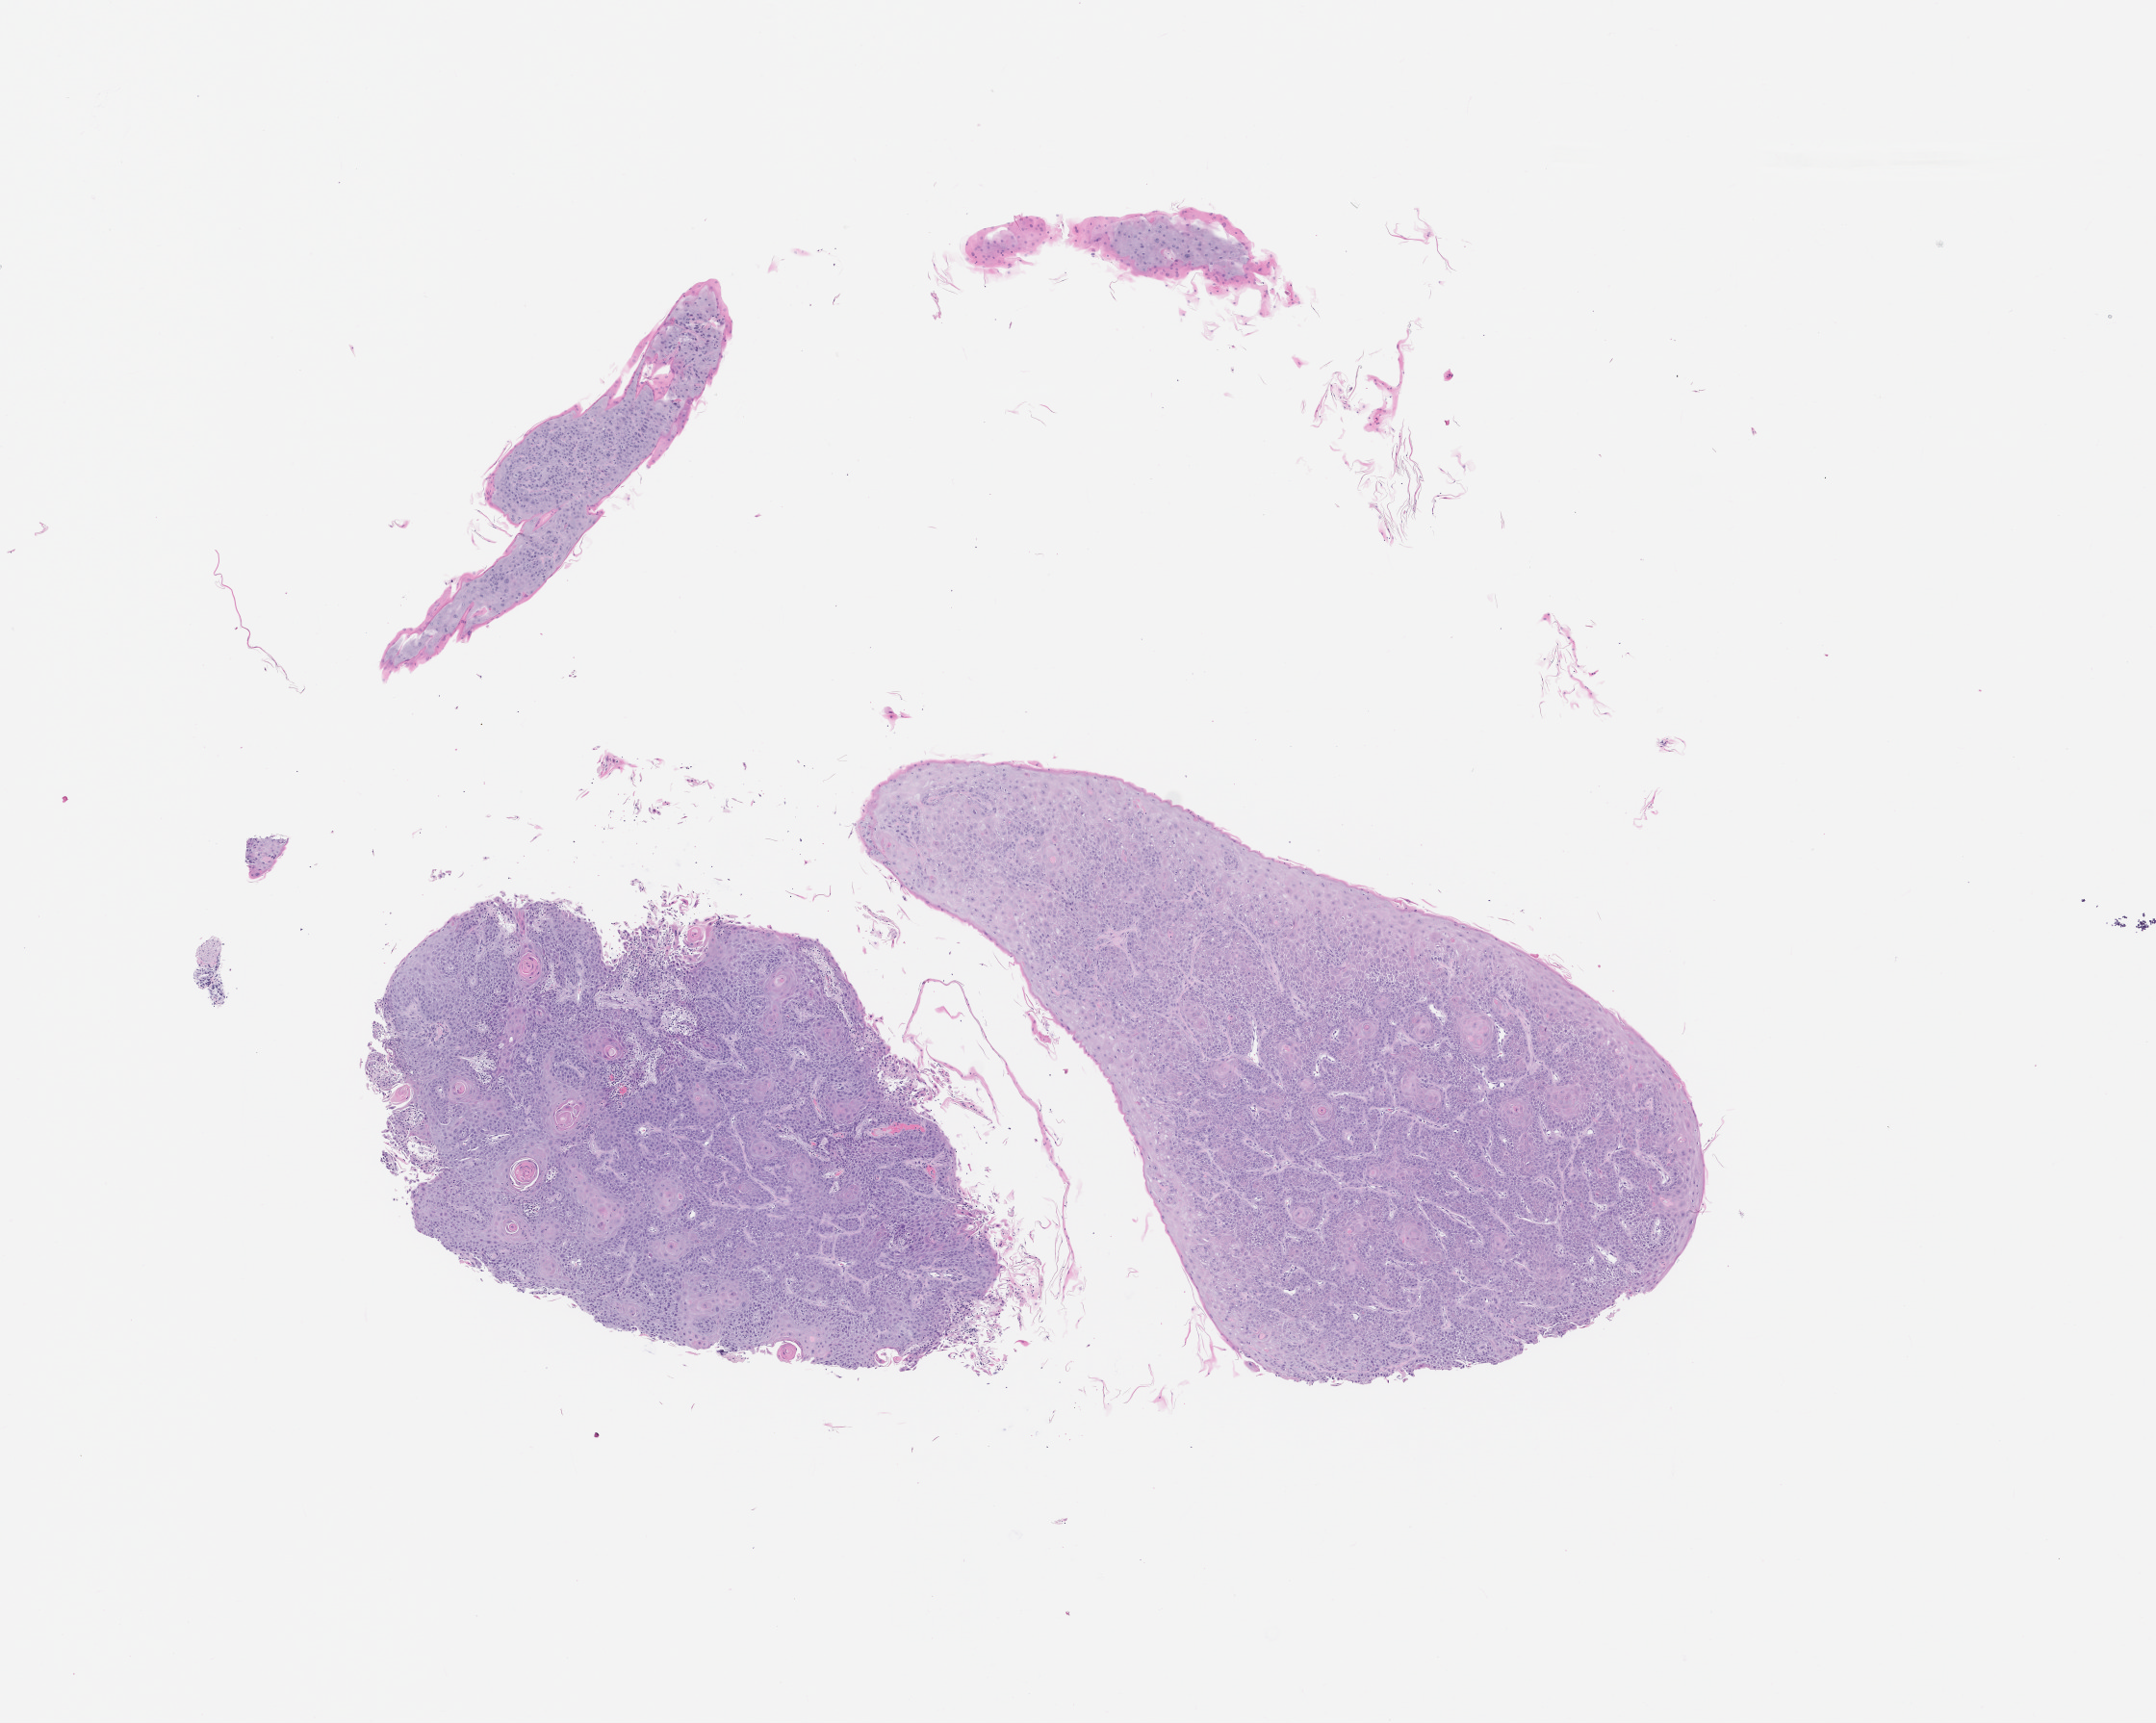
Hematoxylin and eosin (H&E) whole-slide image of a patient-derived xenograft (PDX) tumor grown in a mouse, passage 0, whole scanned area (about 9.0 x 7.2 mm) shown as a low-resolution overview. Formalin-fixed, paraffin-embedded (FFPE) tissue. Tumor site category: bladder.
Originating patient diagnosis: Transitional Cell Carcinoma.